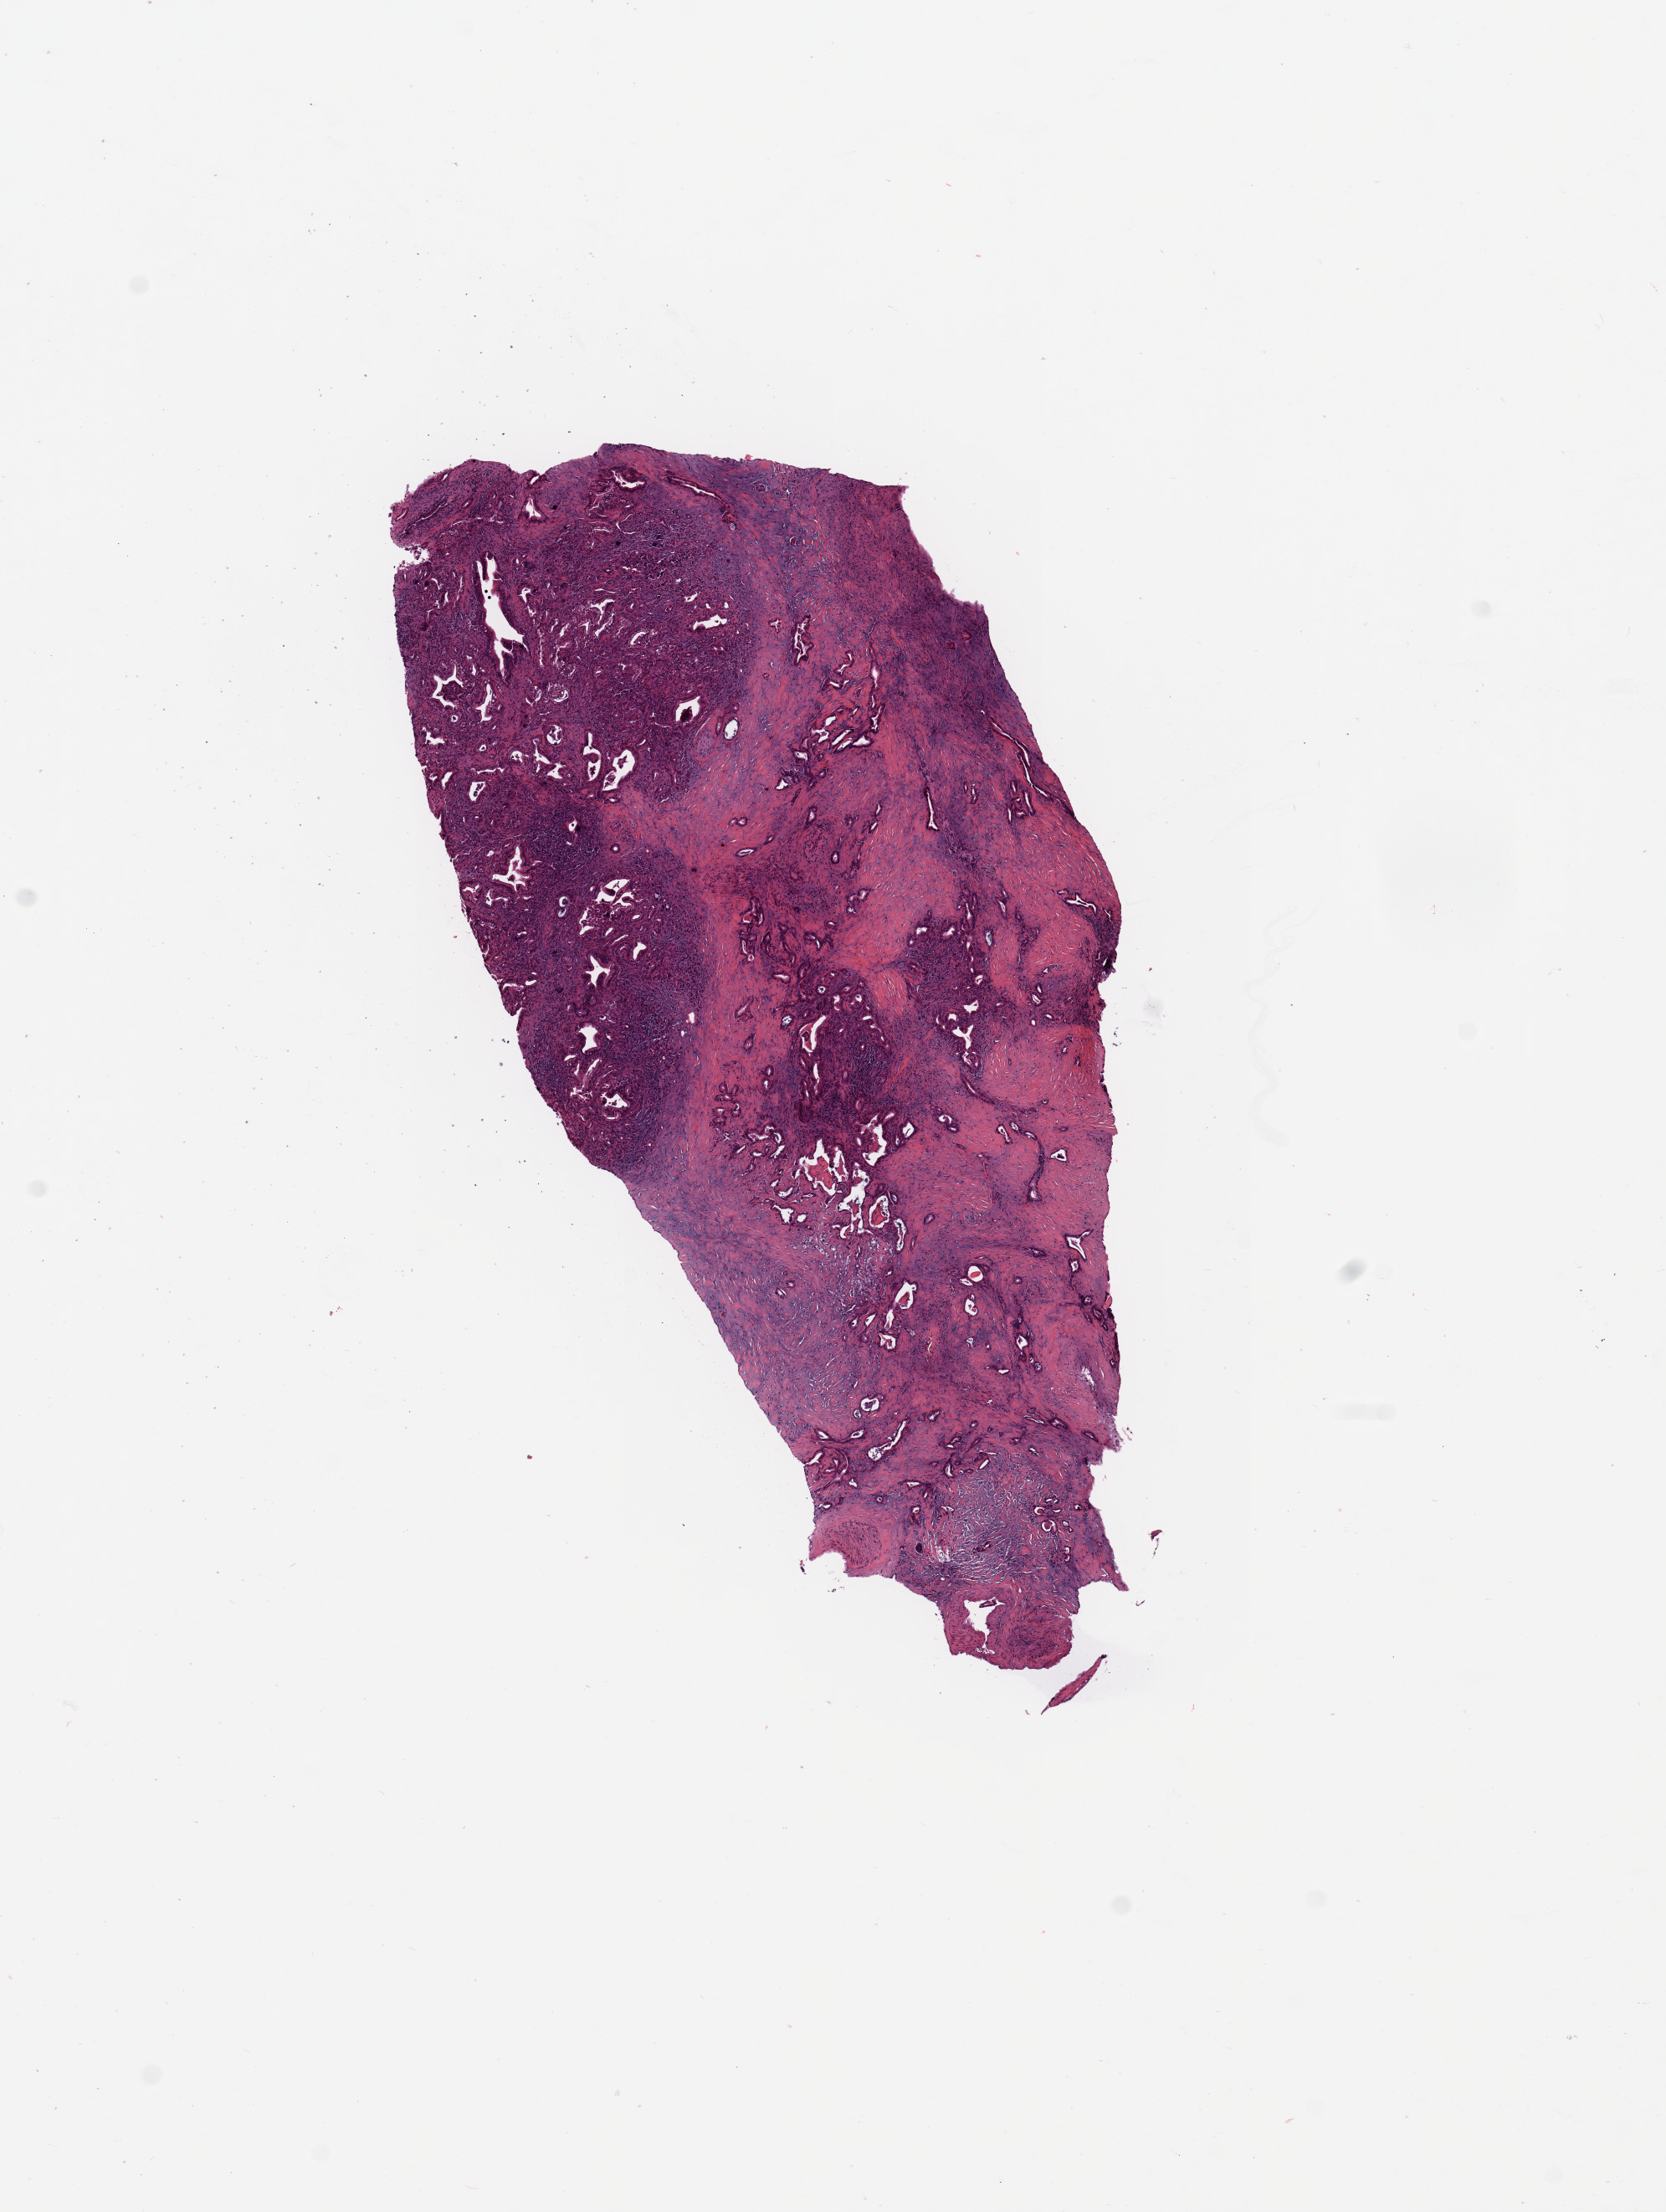
Whole-slide histology image, H&E — shown as a low-resolution overview of the whole scanned area (about 7.9 x 10.5 mm, slide scanned at 20x), pancreas, tissue type not recorded.
Patient diagnosis (cohort enrolment): ductal adenocarcinoma (pancreas).